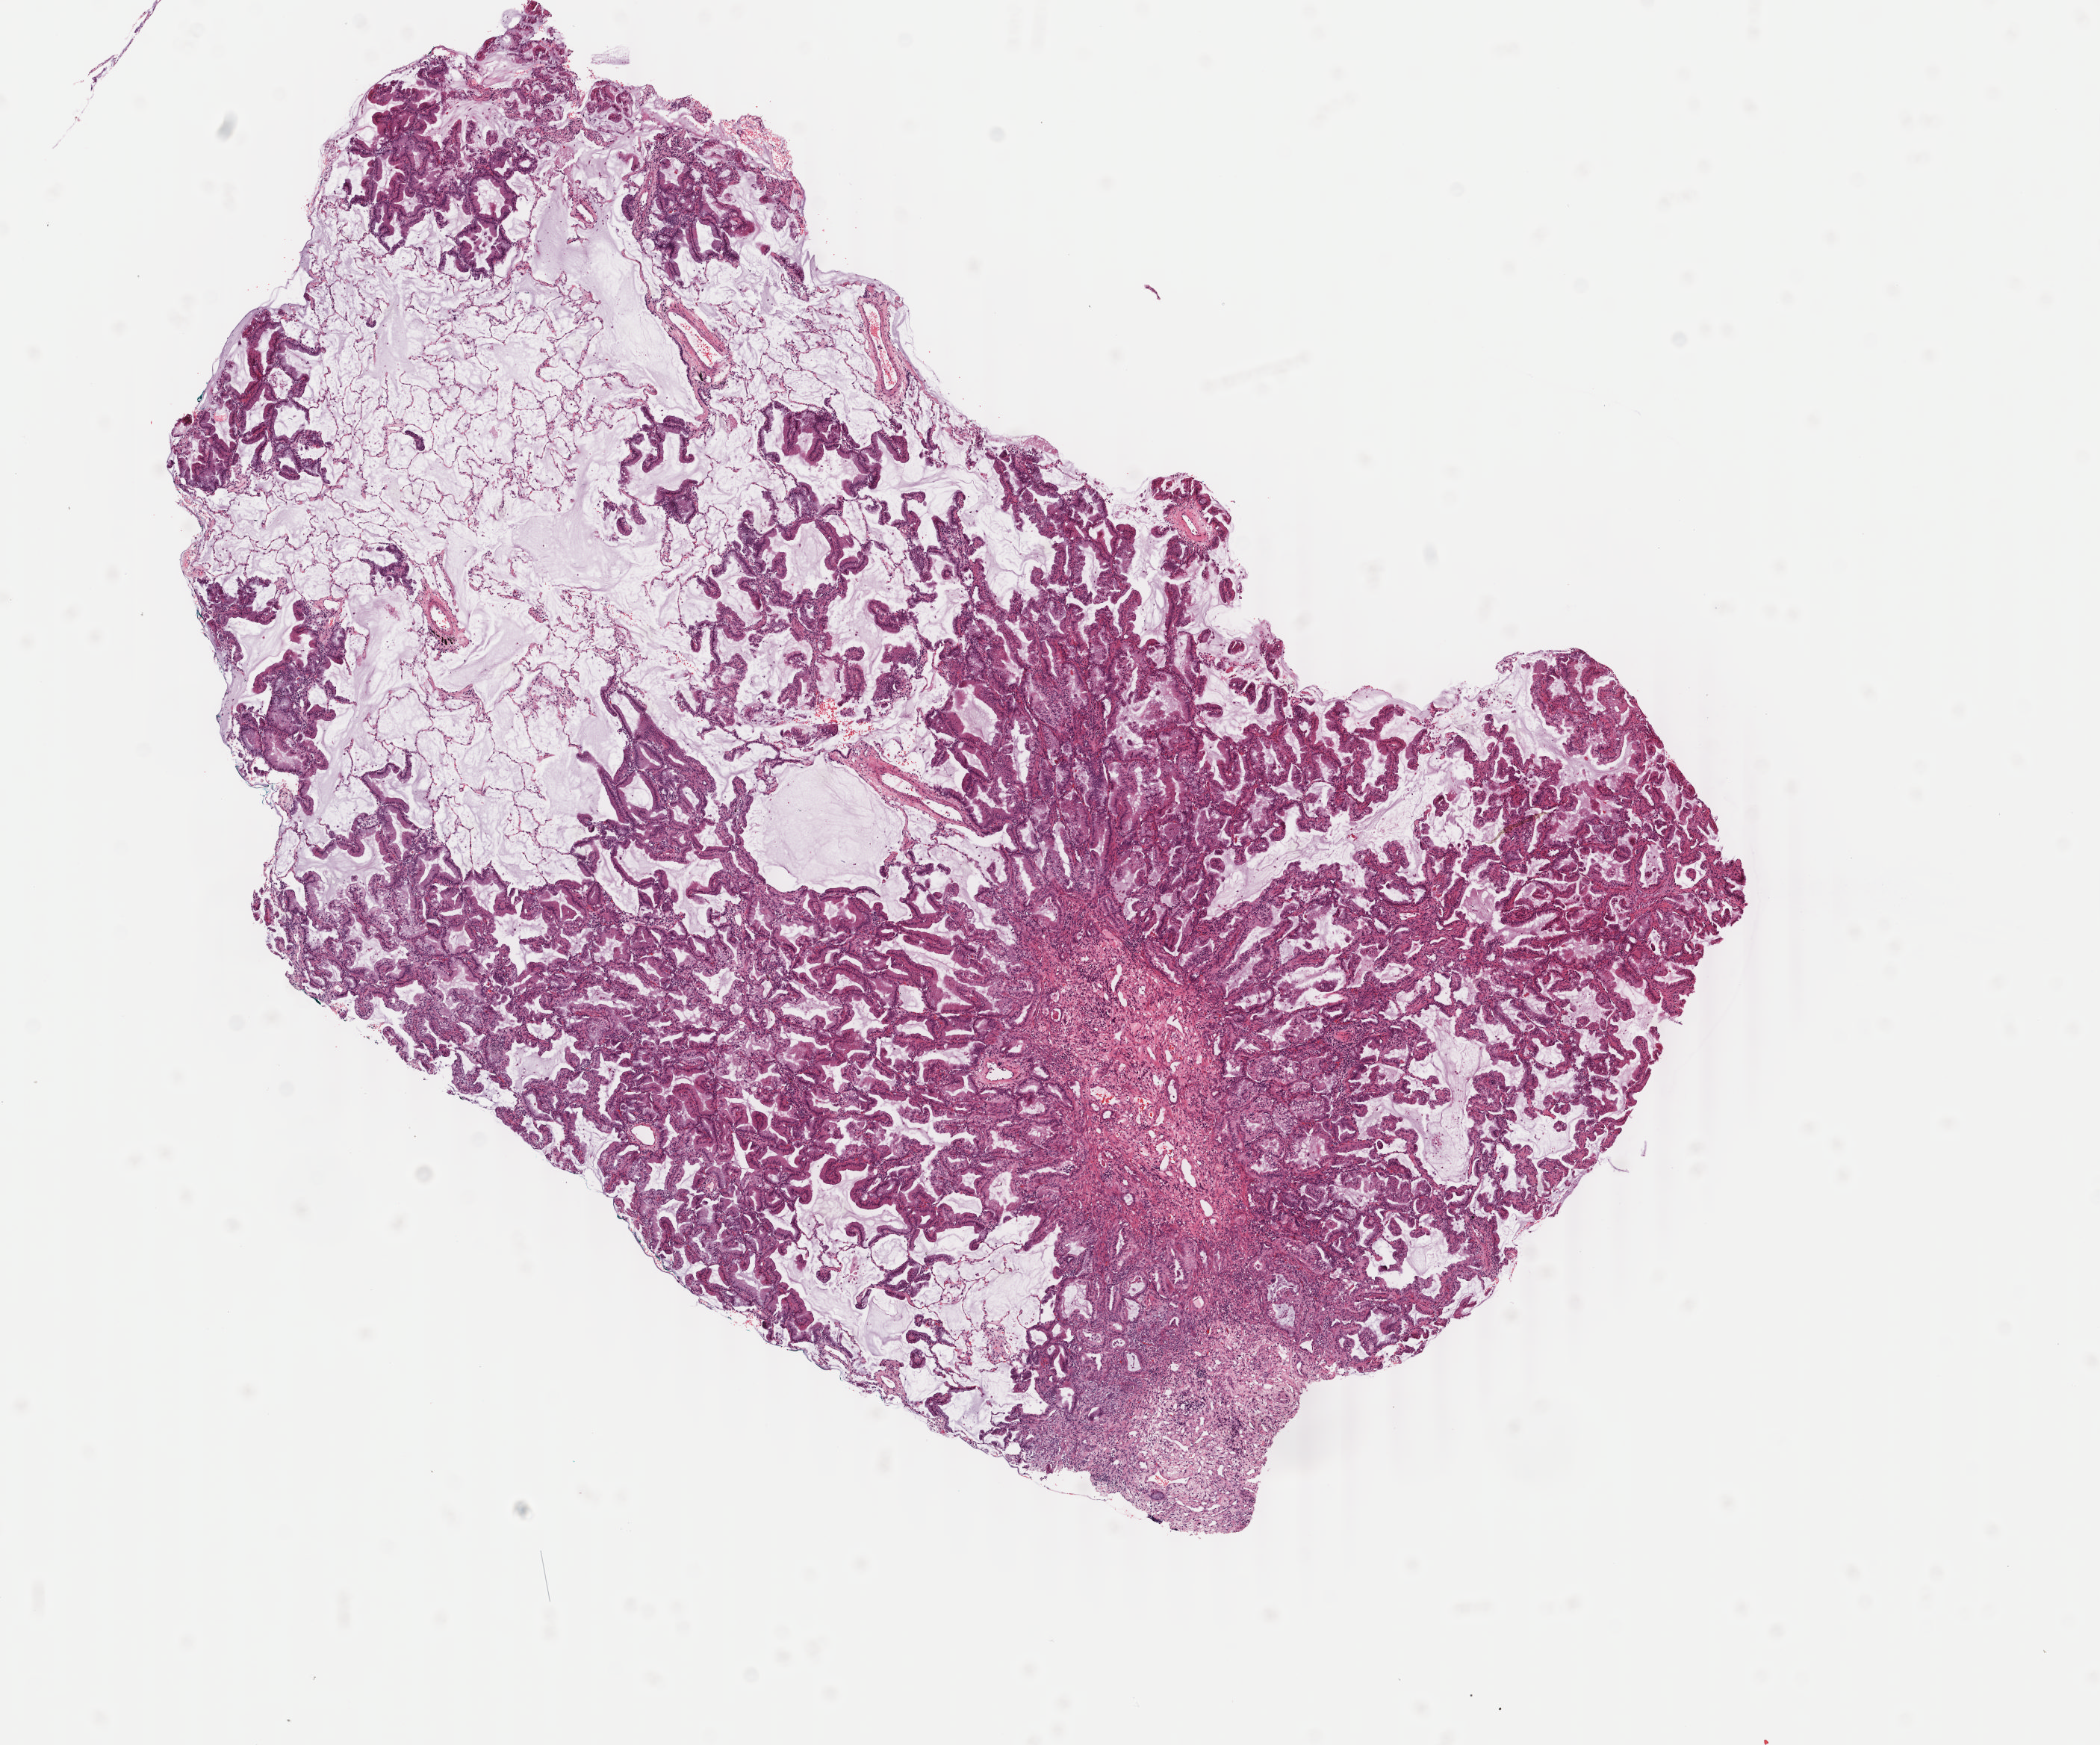
Digitized H&E-stained tissue section (whole slide) — low-resolution overview of the scanned area, about 11.2 x 9.3 mm (slide scanned at 40x), frozen section, primary tumour sample from the lung. Male patient; age at initial diagnosis 64 years. Composition of this section per pathologist review: tumour cells 79%, tumour nuclei 80%, normal cells 0%, stromal cells 20%, necrosis 1%. Infiltration values recorded for this section: lymphocyte infiltration 10%, monocyte infiltration 3%, neutrophil infiltration 1%.
Laterality: left. Diagnosis: Mucinous adenocarcinoma (lower lobe, lung). AJCC pathologic stage: IIB (7th edition).